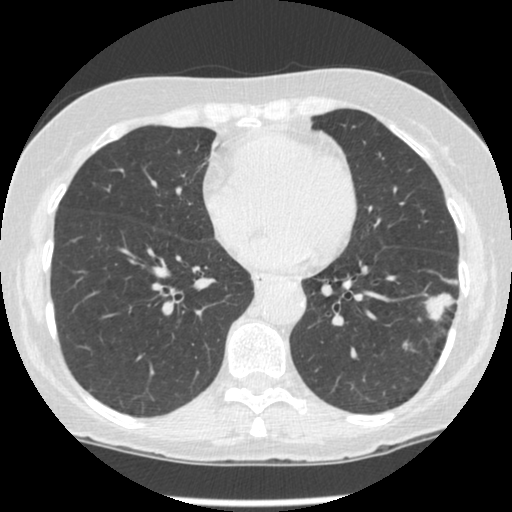
Low-dose screening chest CT, one axial slice. Slice 99 of 247 in the series (ordered by position). Reconstruction kernel STANDARD. Lung window (W 1500 / L -600 HU). 1.25 mm slice thickness. 512 × 512 image matrix, field of view 303 × 303 mm.
Structures marked on this image (outlined manually by an expert reader):
- lesion 1 (tumor, lower lobe of left lung): box from (x=425, y=293) to (x=455, y=321) px